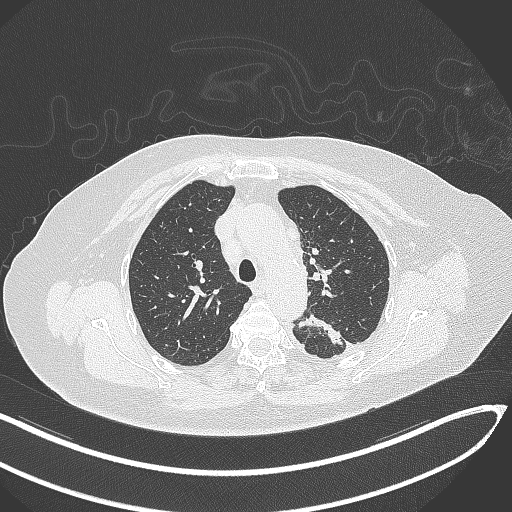
Chest CT, one axial slice; position 228 of 270 along the scan axis; reconstruction kernel B70f; 120 kVp; lung window (W 1500 / L -600 HU); 1 mm slice thickness; 512 × 512 image matrix, field of view 400 × 400 mm. Female patient, age 76 years. From the clinical record (not read from this slice): clinical TNM (as recorded): T1c N0 M0.
Structures marked on this image (bounding box drawn by a radiologist):
- lung tumour (recorded histology: adenocarcinoma): bounding box (x1, y1, x2, y2) in pixels: (294, 307, 350, 351)